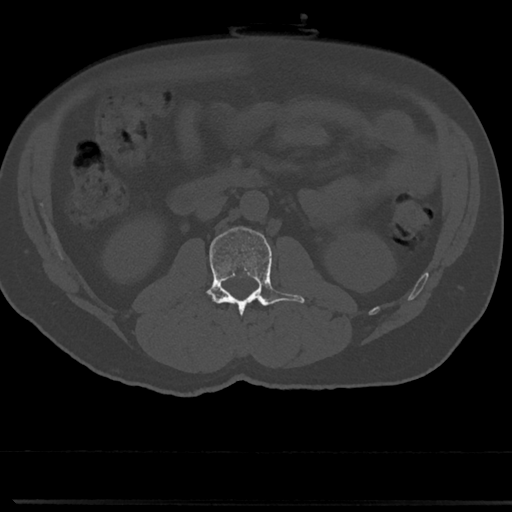
CT including the spine, one axial slice; position 15 of 817 along the scan axis; reconstruction kernel Br40s/3; bone window (W 1800 / L 400 HU); 512 × 512 image matrix. Patient: male, 61 years. From the clinical record (not read from this slice): primary cancer: prostate.
Annotated regions visible in this slice (semi-automatic segmentation, software-assisted and operator-edited):
- L2 vertebra: box from (x=208, y=227) to (x=304, y=322) px